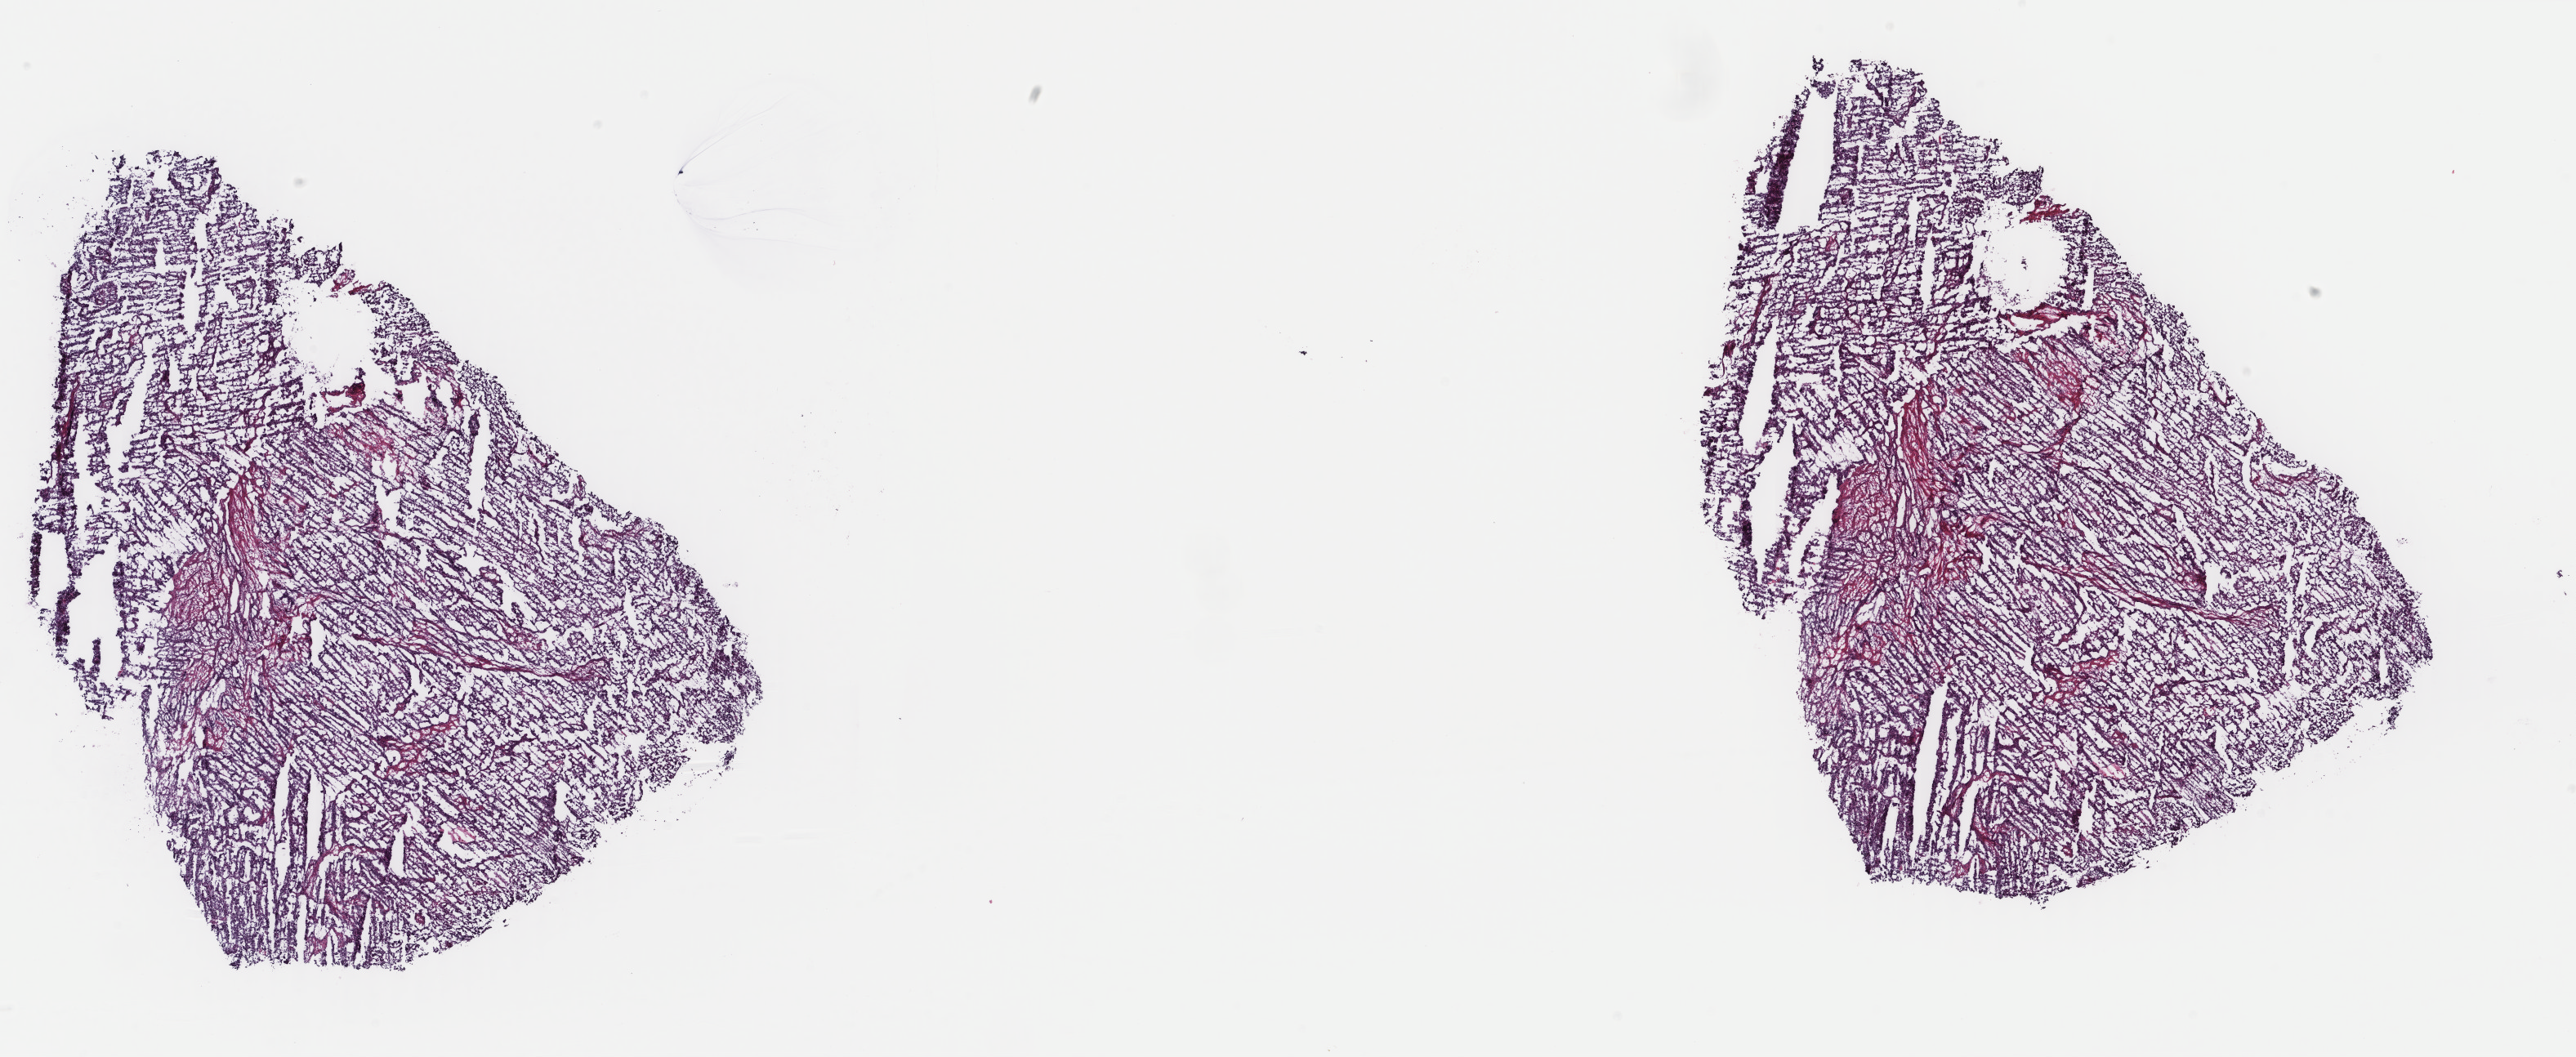
Whole-slide histology image, H&E — whole scanned area (about 25.0 x 10.3 mm, slide scanned at 40x) shown as a low-resolution overview; frozen section; sample: primary tumour, uterus. Patient: female, age at initial diagnosis 53 years. Histologic grade: G3 (poorly differentiated). Composition of this section per pathologist review: tumour cells 60%, tumour nuclei 80%, normal cells 0%, stromal cells 20%, necrosis 20%. Inflammatory infiltration, as recorded: lymphocyte infiltration 20%, monocyte infiltration 0%, neutrophil infiltration 20%.
- lymph nodes positive (case pathology): 0 of 7 examined
- FIGO stage: IA
- pathologic diagnosis: Endometrioid adenocarcinoma, NOS (endometrium)